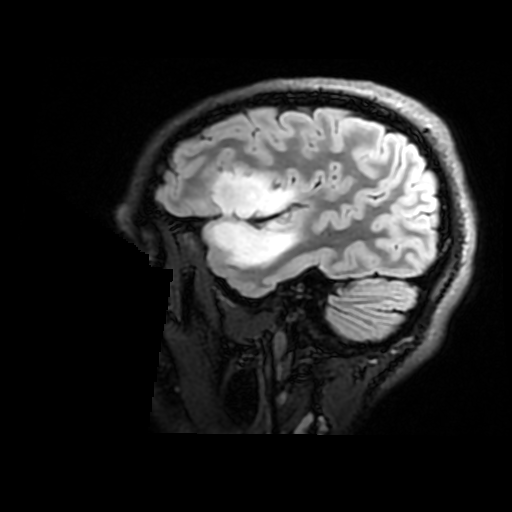
Brain MRI from a brain-tumour surgery series, one sagittal slice; position 134 of 176 along the scan axis; T2 FLAIR; 1 mm slice thickness; 512 × 512 image matrix, field of view 240 × 240 mm. From the clinical record (not read from this slice): histopathology: Astrocytoma; WHO grade: 2; IDH mutation: yes; tumour location: Right Insular.
Outlined on this slice (manually delineated by an expert):
- tumour: bounding box <212,171,301,269> (left, top, right, bottom; pixels)